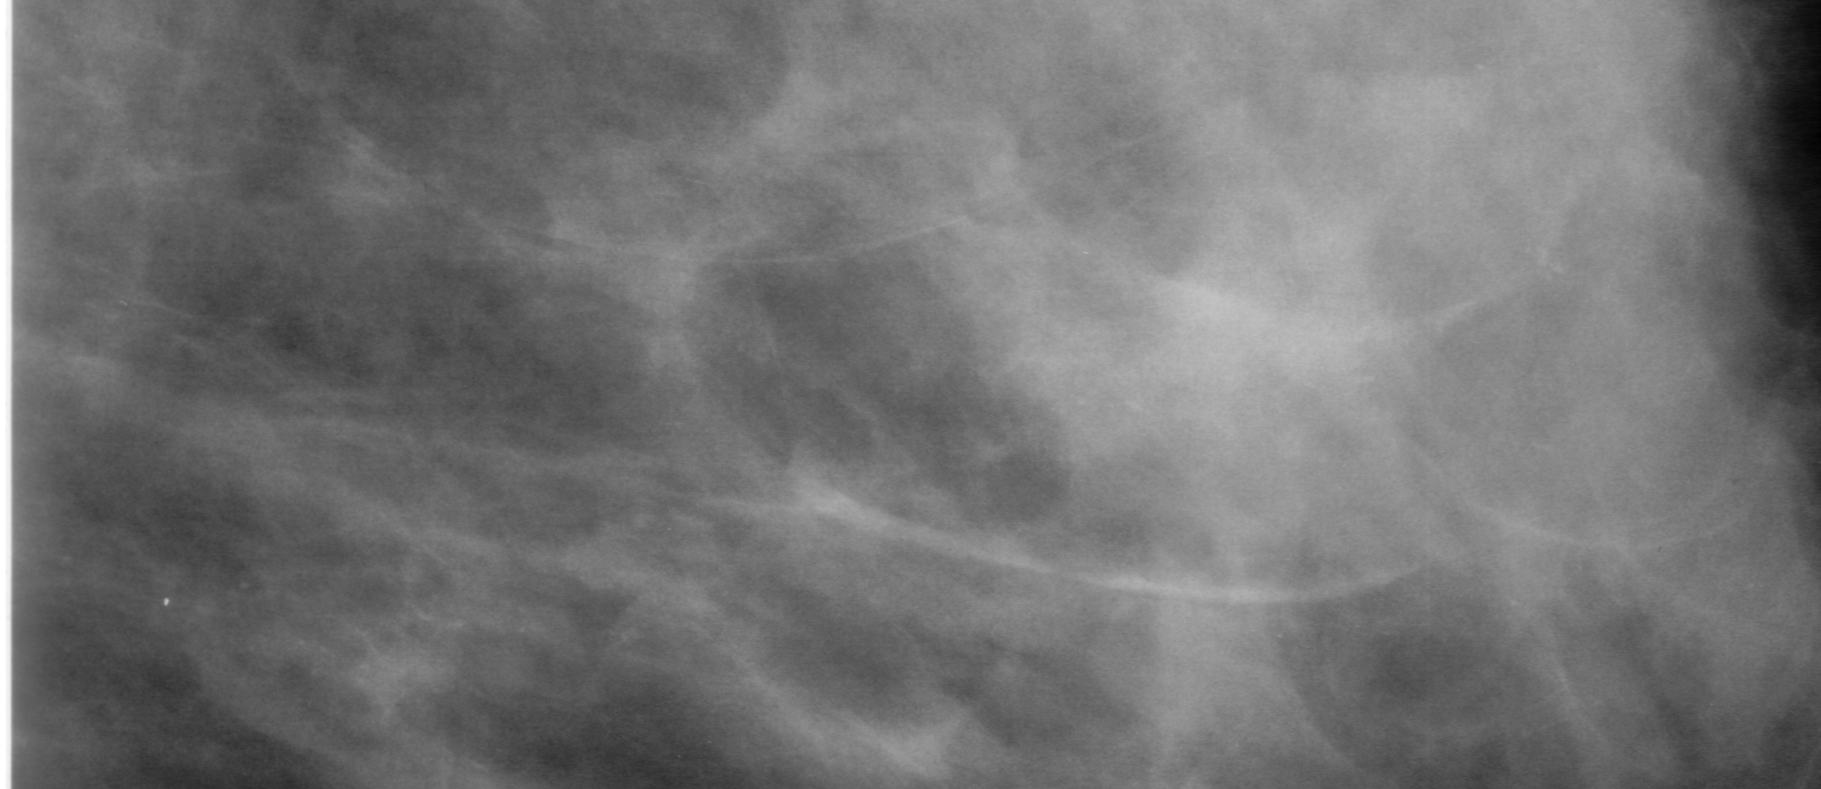
Region of interest cut from a scanned film mammogram (one marked finding), left breast, MLO view, BI-RADS breast density category 3 (scale 1–4).
Finding: calcifications, morphology amorphous, distribution segmental; BI-RADS assessment category 0 (incomplete: needs additional imaging); subtlety rating 1 on a 1 (subtle) to 5 (obvious) scale; pathology result (as recorded, not read from the image): benign.